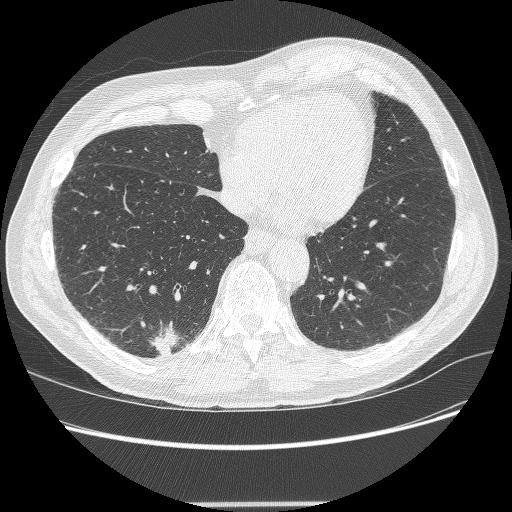
Axial slice from a low-dose chest CT screening exam. Second annual screen. Lung window (W 1500 / L -600 HU). 1.25 mm slice thickness. Male participant, aged 71 years at enrolment.
Expert-annotated lung lesion, bounding box (x1, y1, x2, y2) in pixels: (137, 323, 189, 364). The screening reader recorded 5 non-calcified nodules or masses ≥4 mm on this exam (right lower lobe, right lower lobe, right upper lobe, right upper lobe, right upper lobe); which of them this box marks is not recorded. Participant outcome: lung cancer diagnosed 7 days after this screen — squamous cell carcinoma, NOS, right lower lobe, moderately differentiated (G2), stage IA (AJCC 6th edition), 27 mm at pathology.